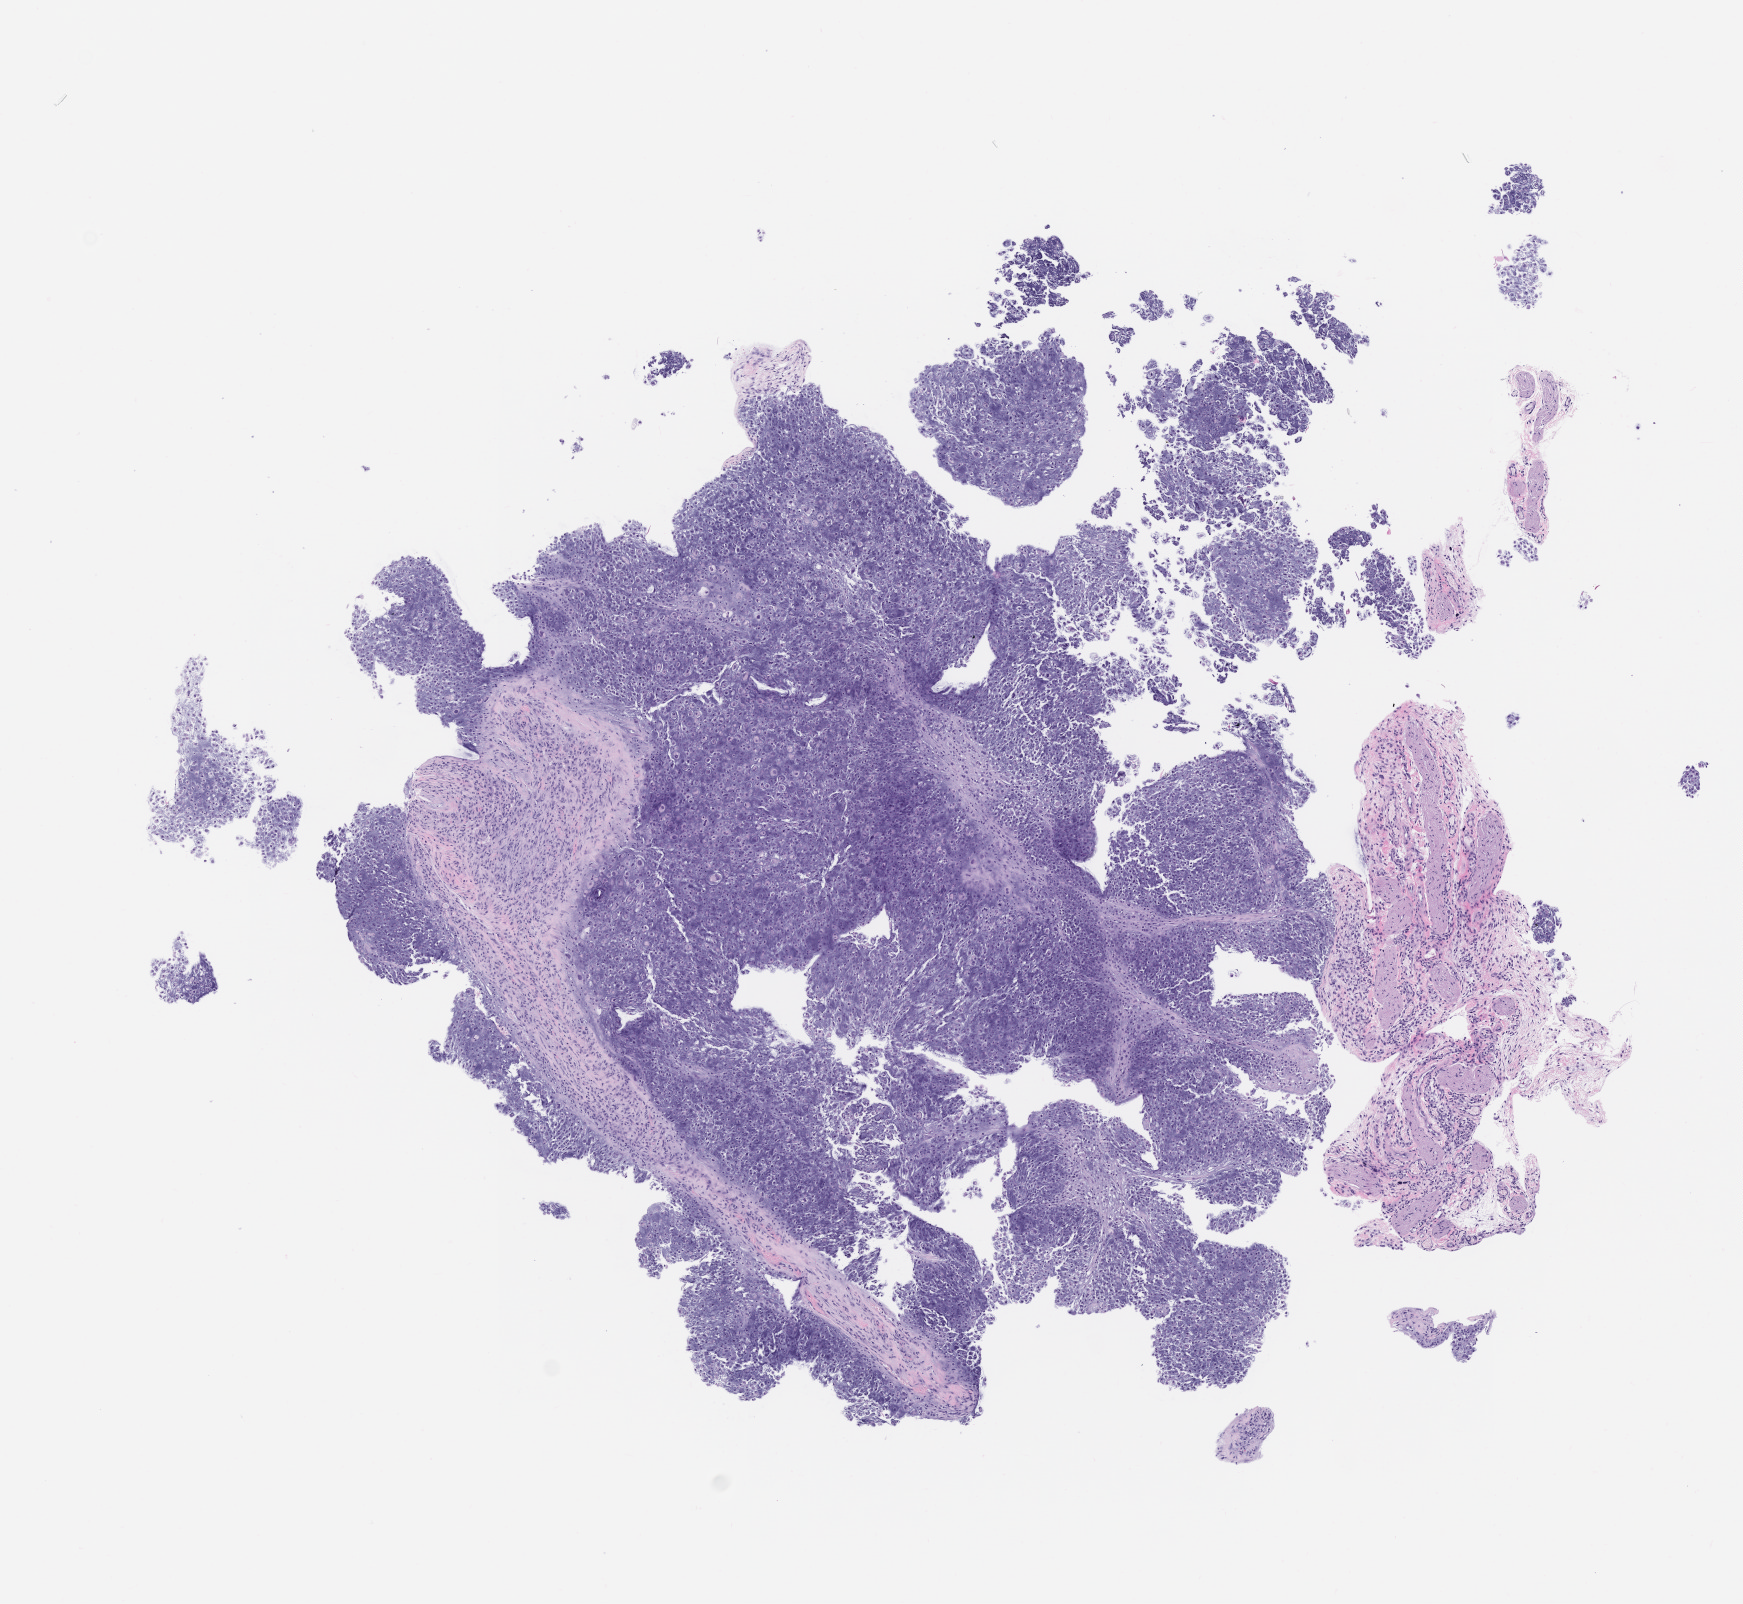
Whole-slide image, hematoxylin and eosin (H&E): patient-derived xenograft (human tumor grown in a mouse), passage 1 — low-resolution overview of the scanned area, about 7.0 x 6.5 mm. Formalin-fixed, paraffin-embedded (FFPE) tissue. Originating tumor site category: musculoskeletal.
Originating patient diagnosis: Chondrosarcoma.